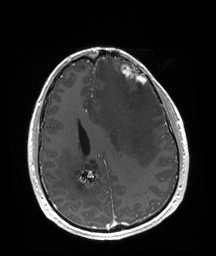
Brain MRI from a brain-tumour surgery series, one axial slice. Slice 68 of 192 in the series (ordered by position). T1-weighted post-contrast. 1 mm slice thickness. 216 × 256 image matrix. Case-level facts recorded for this patient, not image findings: tumour location: Left Frontal.
Structures marked on this image (manually delineated by an expert):
- tumour: bounding box [x1, y1, x2, y2] px = [121, 65, 147, 89]